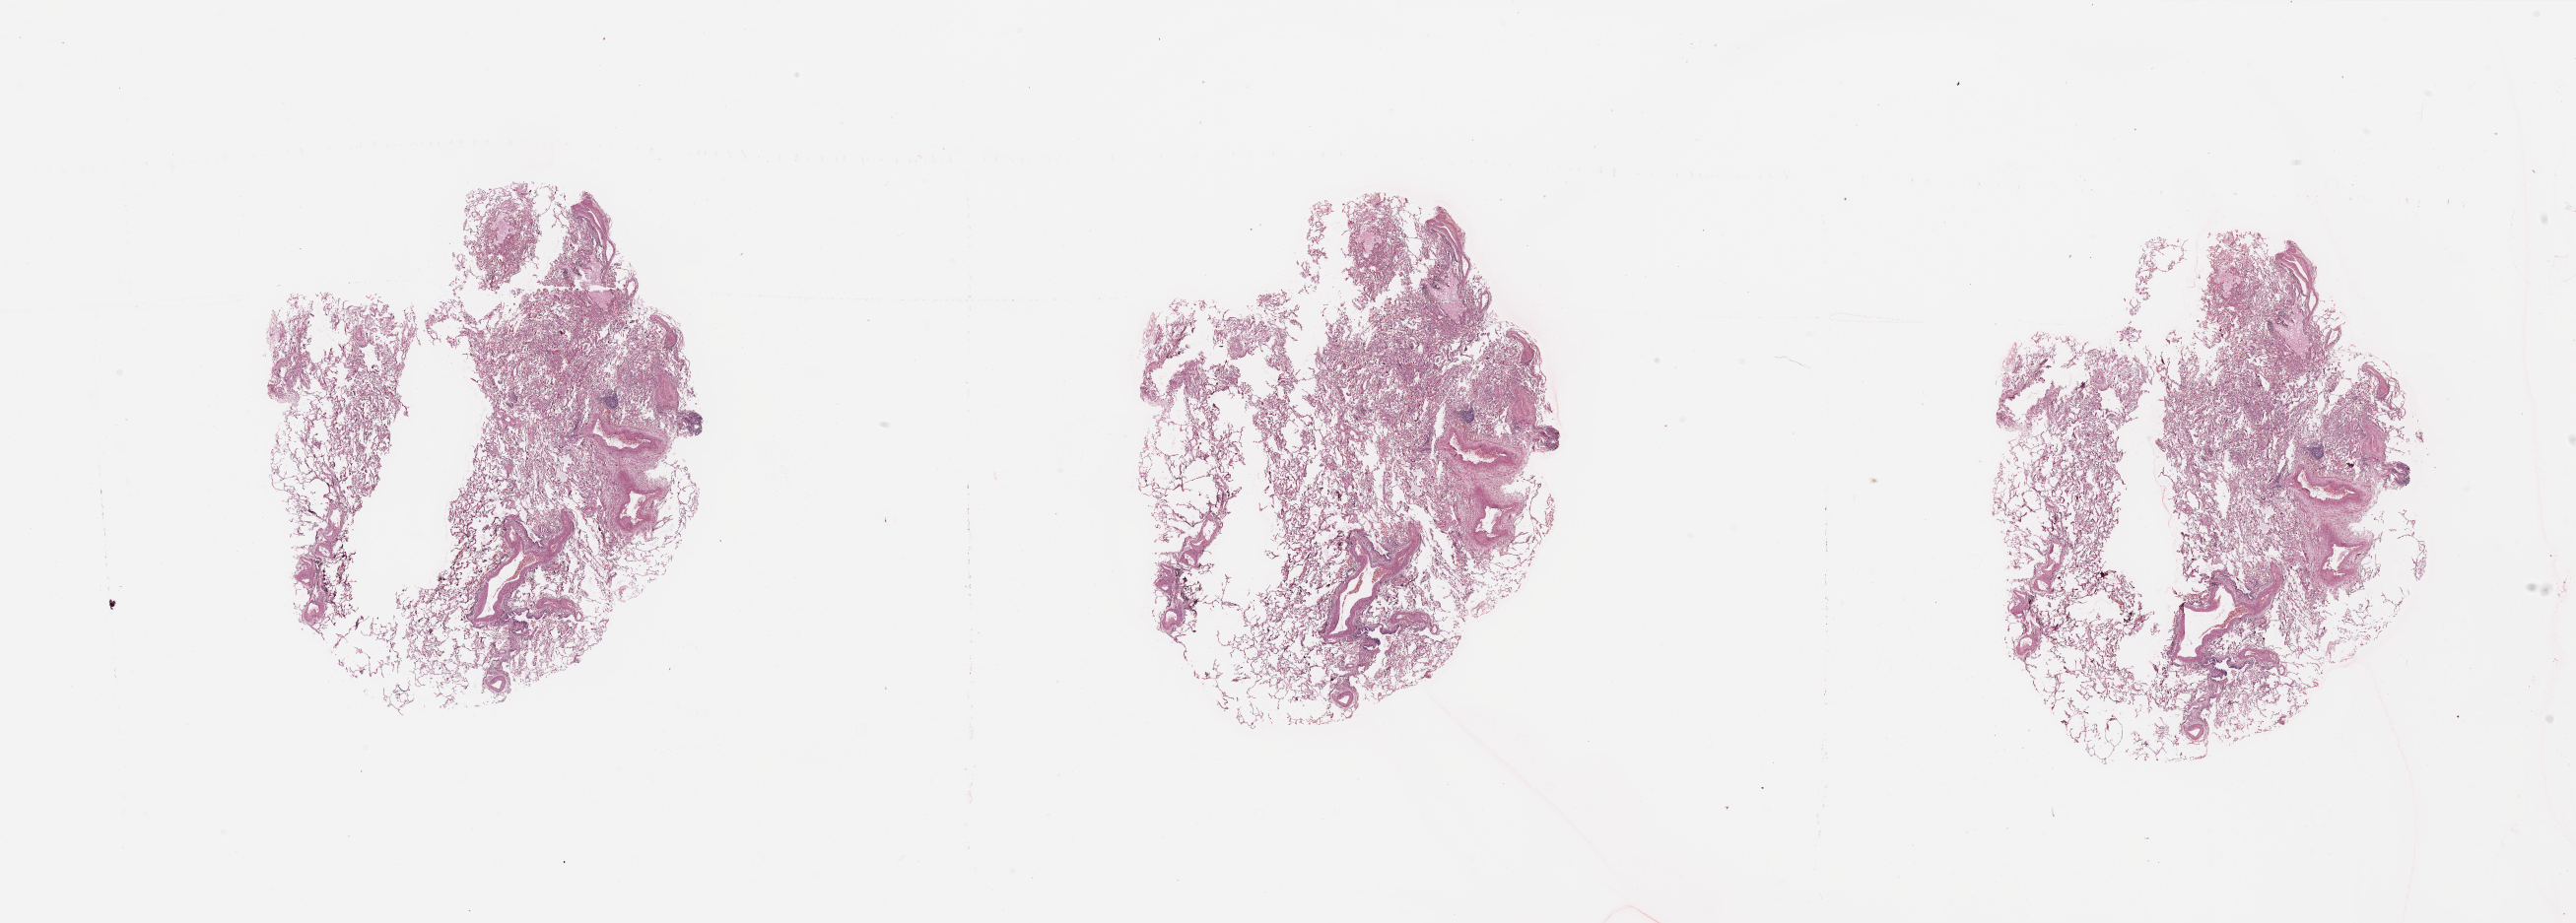
Whole-slide histology image, H&E, a low-resolution overview of the entire scanned area, about 41.3 x 14.8 mm (slide scanned at 20x), normal (non-tumour) tissue sample, sampled site: lung. Female, 73 y/o.
This section: normal (non-tumour) tissue from the same patient. Patient diagnosis: Adenocarcinoma, NOS.